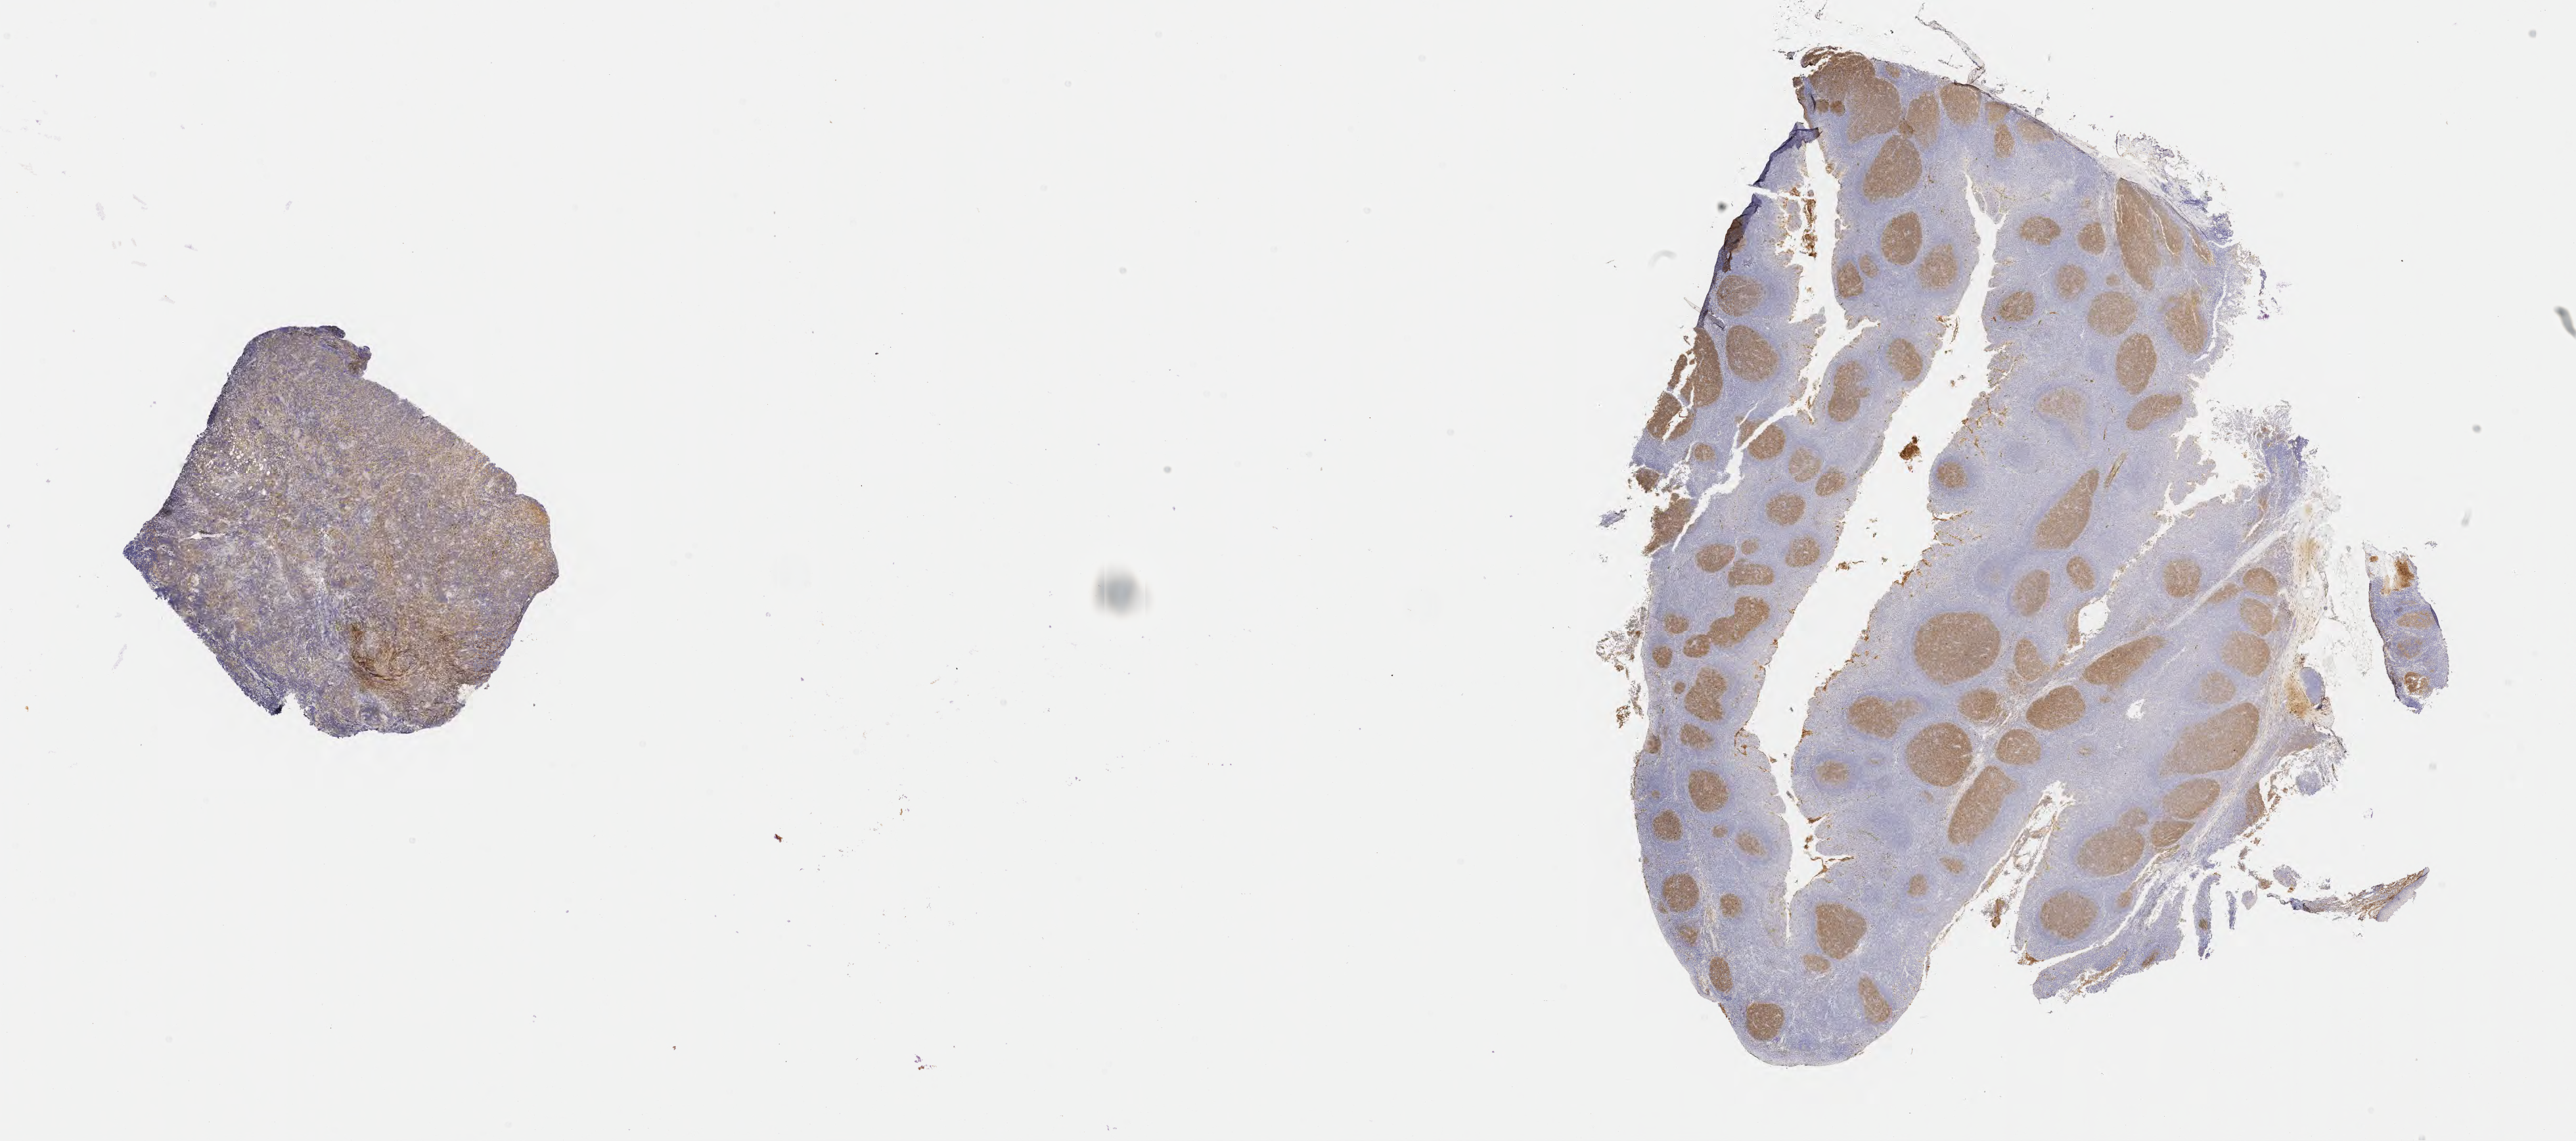
Immunohistochemistry (IHC) whole-slide image stained for CD10, whole scanned area (about 31.7 x 14.0 mm) shown as a low-resolution overview, tumor tissue, anatomic site: buccal mucosa. Patient: male, age at initial diagnosis 7 years.
Diagnosis: Burkitt lymphoma, NOS.